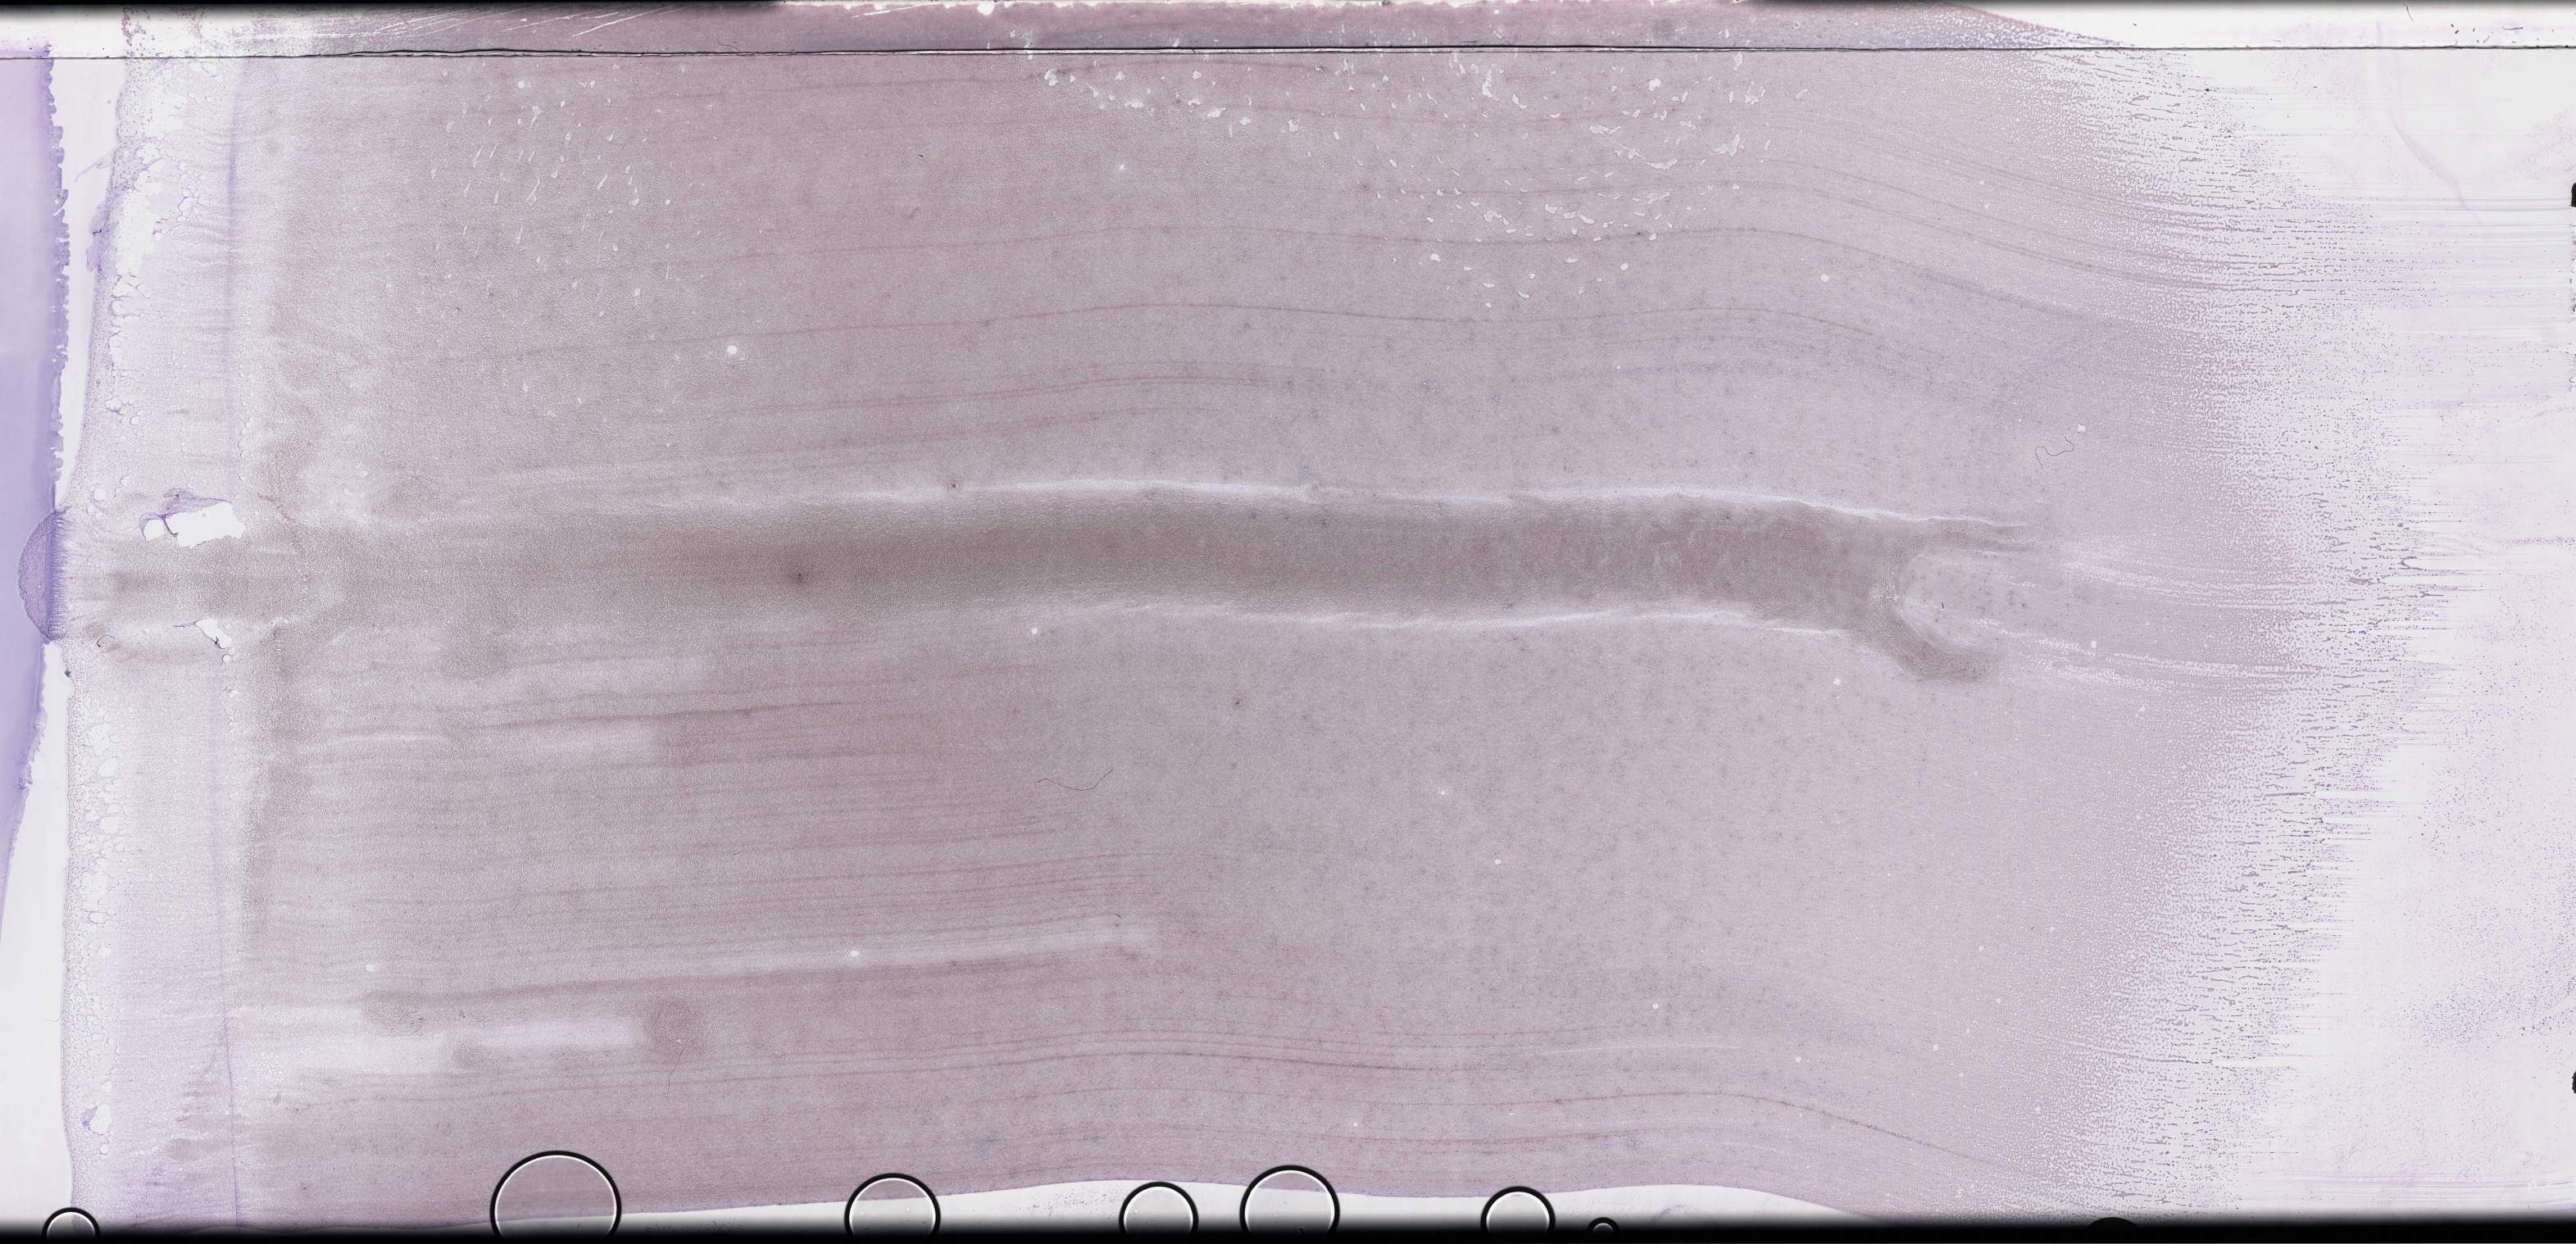
Wright-Giemsa-stained whole blood smear, whole-slide image, a low-resolution overview of the entire scanned area, about 50.8 x 24.5 mm, smear from an EDTA sample, collected on treatment. Male patient.
- patient diagnosis: Plasma Cell Myeloma